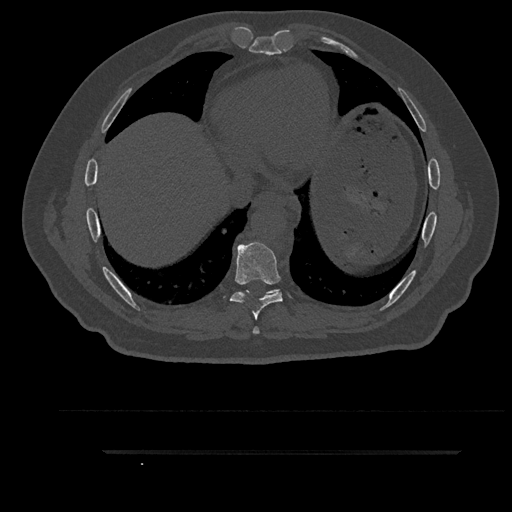
CT including the spine, one axial slice. Position 469 of 797 along the scan axis. Reconstruction kernel Br40s/3. 120 kVp. Bone window (W 1800 / L 400 HU). 512 × 512 image matrix, field of view 432 × 432 mm. Male patient, age 63 years. From the clinical record (not read from this slice): primary cancer: renal.
Outlined on this slice (semi-automatically segmented with operator editing):
- T7 vertebra: bounding box [x1, y1, x2, y2] px = [253, 326, 260, 334]
- T8 vertebra: [230, 242, 283, 320]
- T9 vertebra: [245, 290, 278, 294]